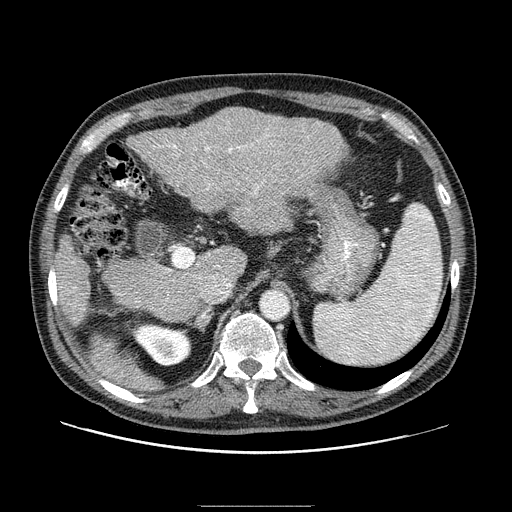
Contrast-enhanced abdominal CT (liver protocol), one axial slice; slice 53 of 99 in the series (ordered by position); reconstruction kernel STANDARD; one of 2 acquisitions stored at this slice position; soft-tissue window (W 400 / L 40 HU); 2.5 mm slice thickness; 512 × 512 image matrix, field of view 400 × 400 mm. From the clinical record (not read from this slice): diagnosis: hepatocellular carcinoma (patient treated with transarterial chemoembolisation; whether this scan precedes or follows treatment is not stated here); TNM stage (as recorded): Stage-II; Child-Pugh class: A; tumour differentiation: well differentiated; tumour nodularity: multinodular.
Structures marked on this image (semi-automatic segmentation, software-assisted and operator-edited):
- liver parenchyma outside the tumour (the mass and vessels are separate outlines, so this box may not span the whole liver): box from (x=50, y=108) to (x=346, y=312) px
- liver vessels: (x=60, y=135)–(x=270, y=288)